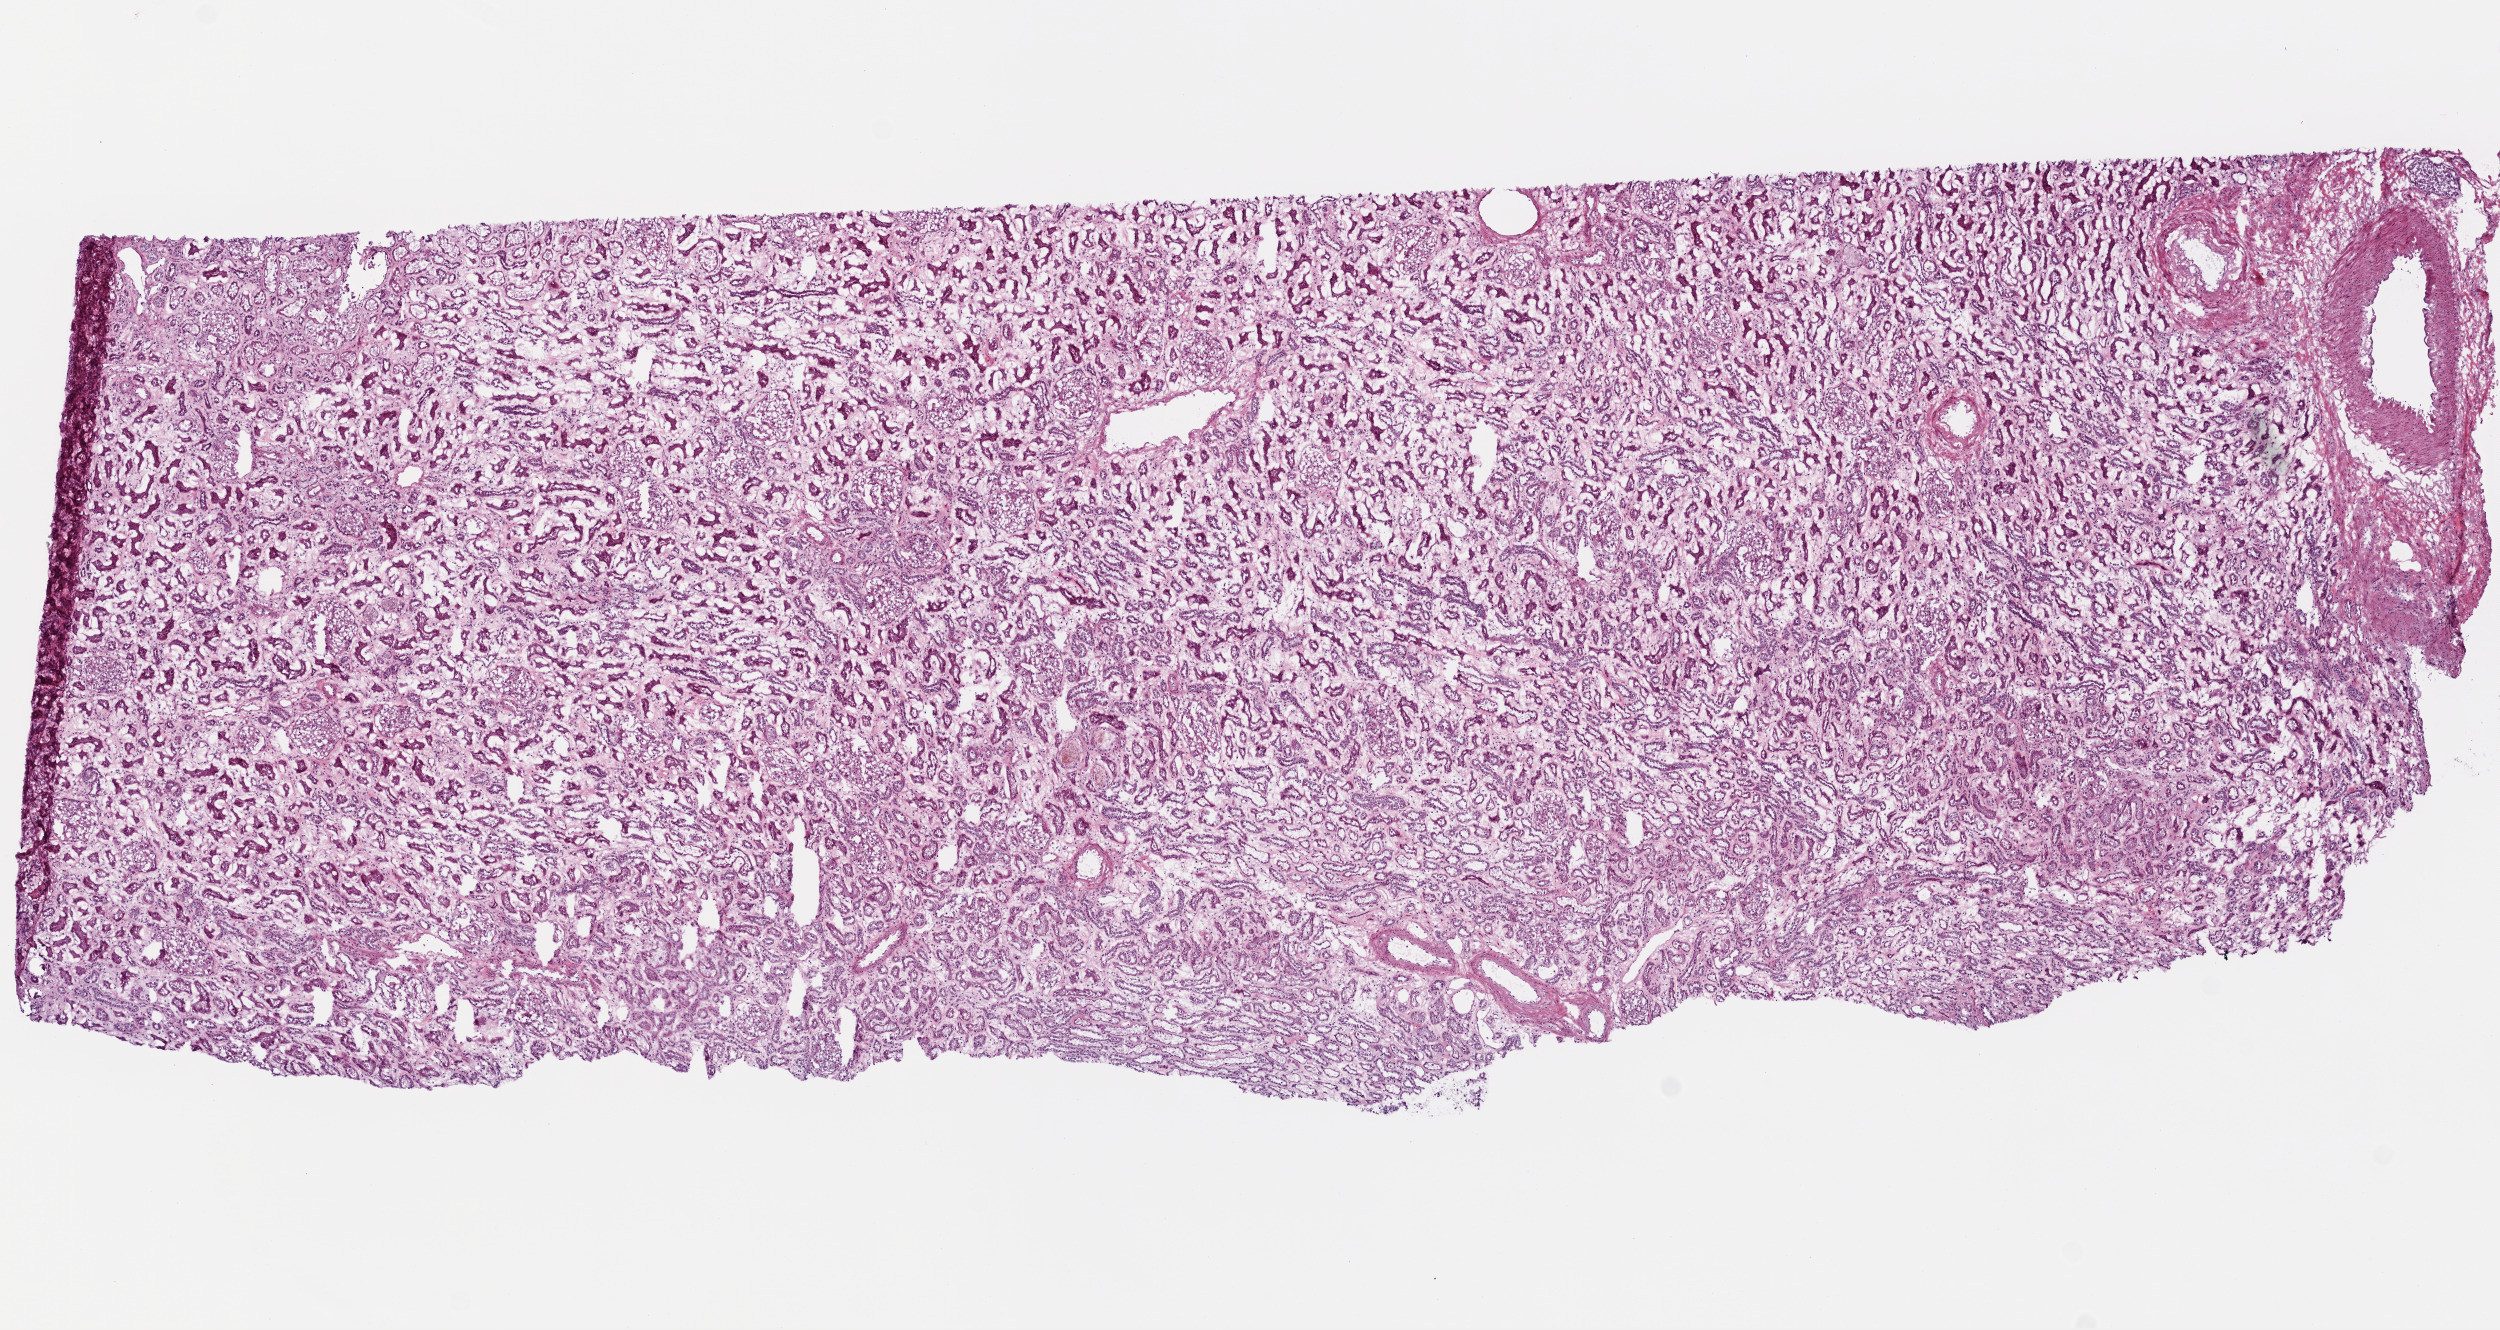
Hematoxylin and eosin (H&E) stained whole-slide image — whole scanned area (about 10.0 x 5.3 mm) shown as a low-resolution overview; frozen section from the top of the tissue portion; sample: solid tissue normal (non-tumour tissue), kidney. Male patient; age at initial diagnosis 51 years.
• this section: solid tissue normal sample (biorepository sample class)
• patient diagnosis: Clear cell adenocarcinoma, NOS